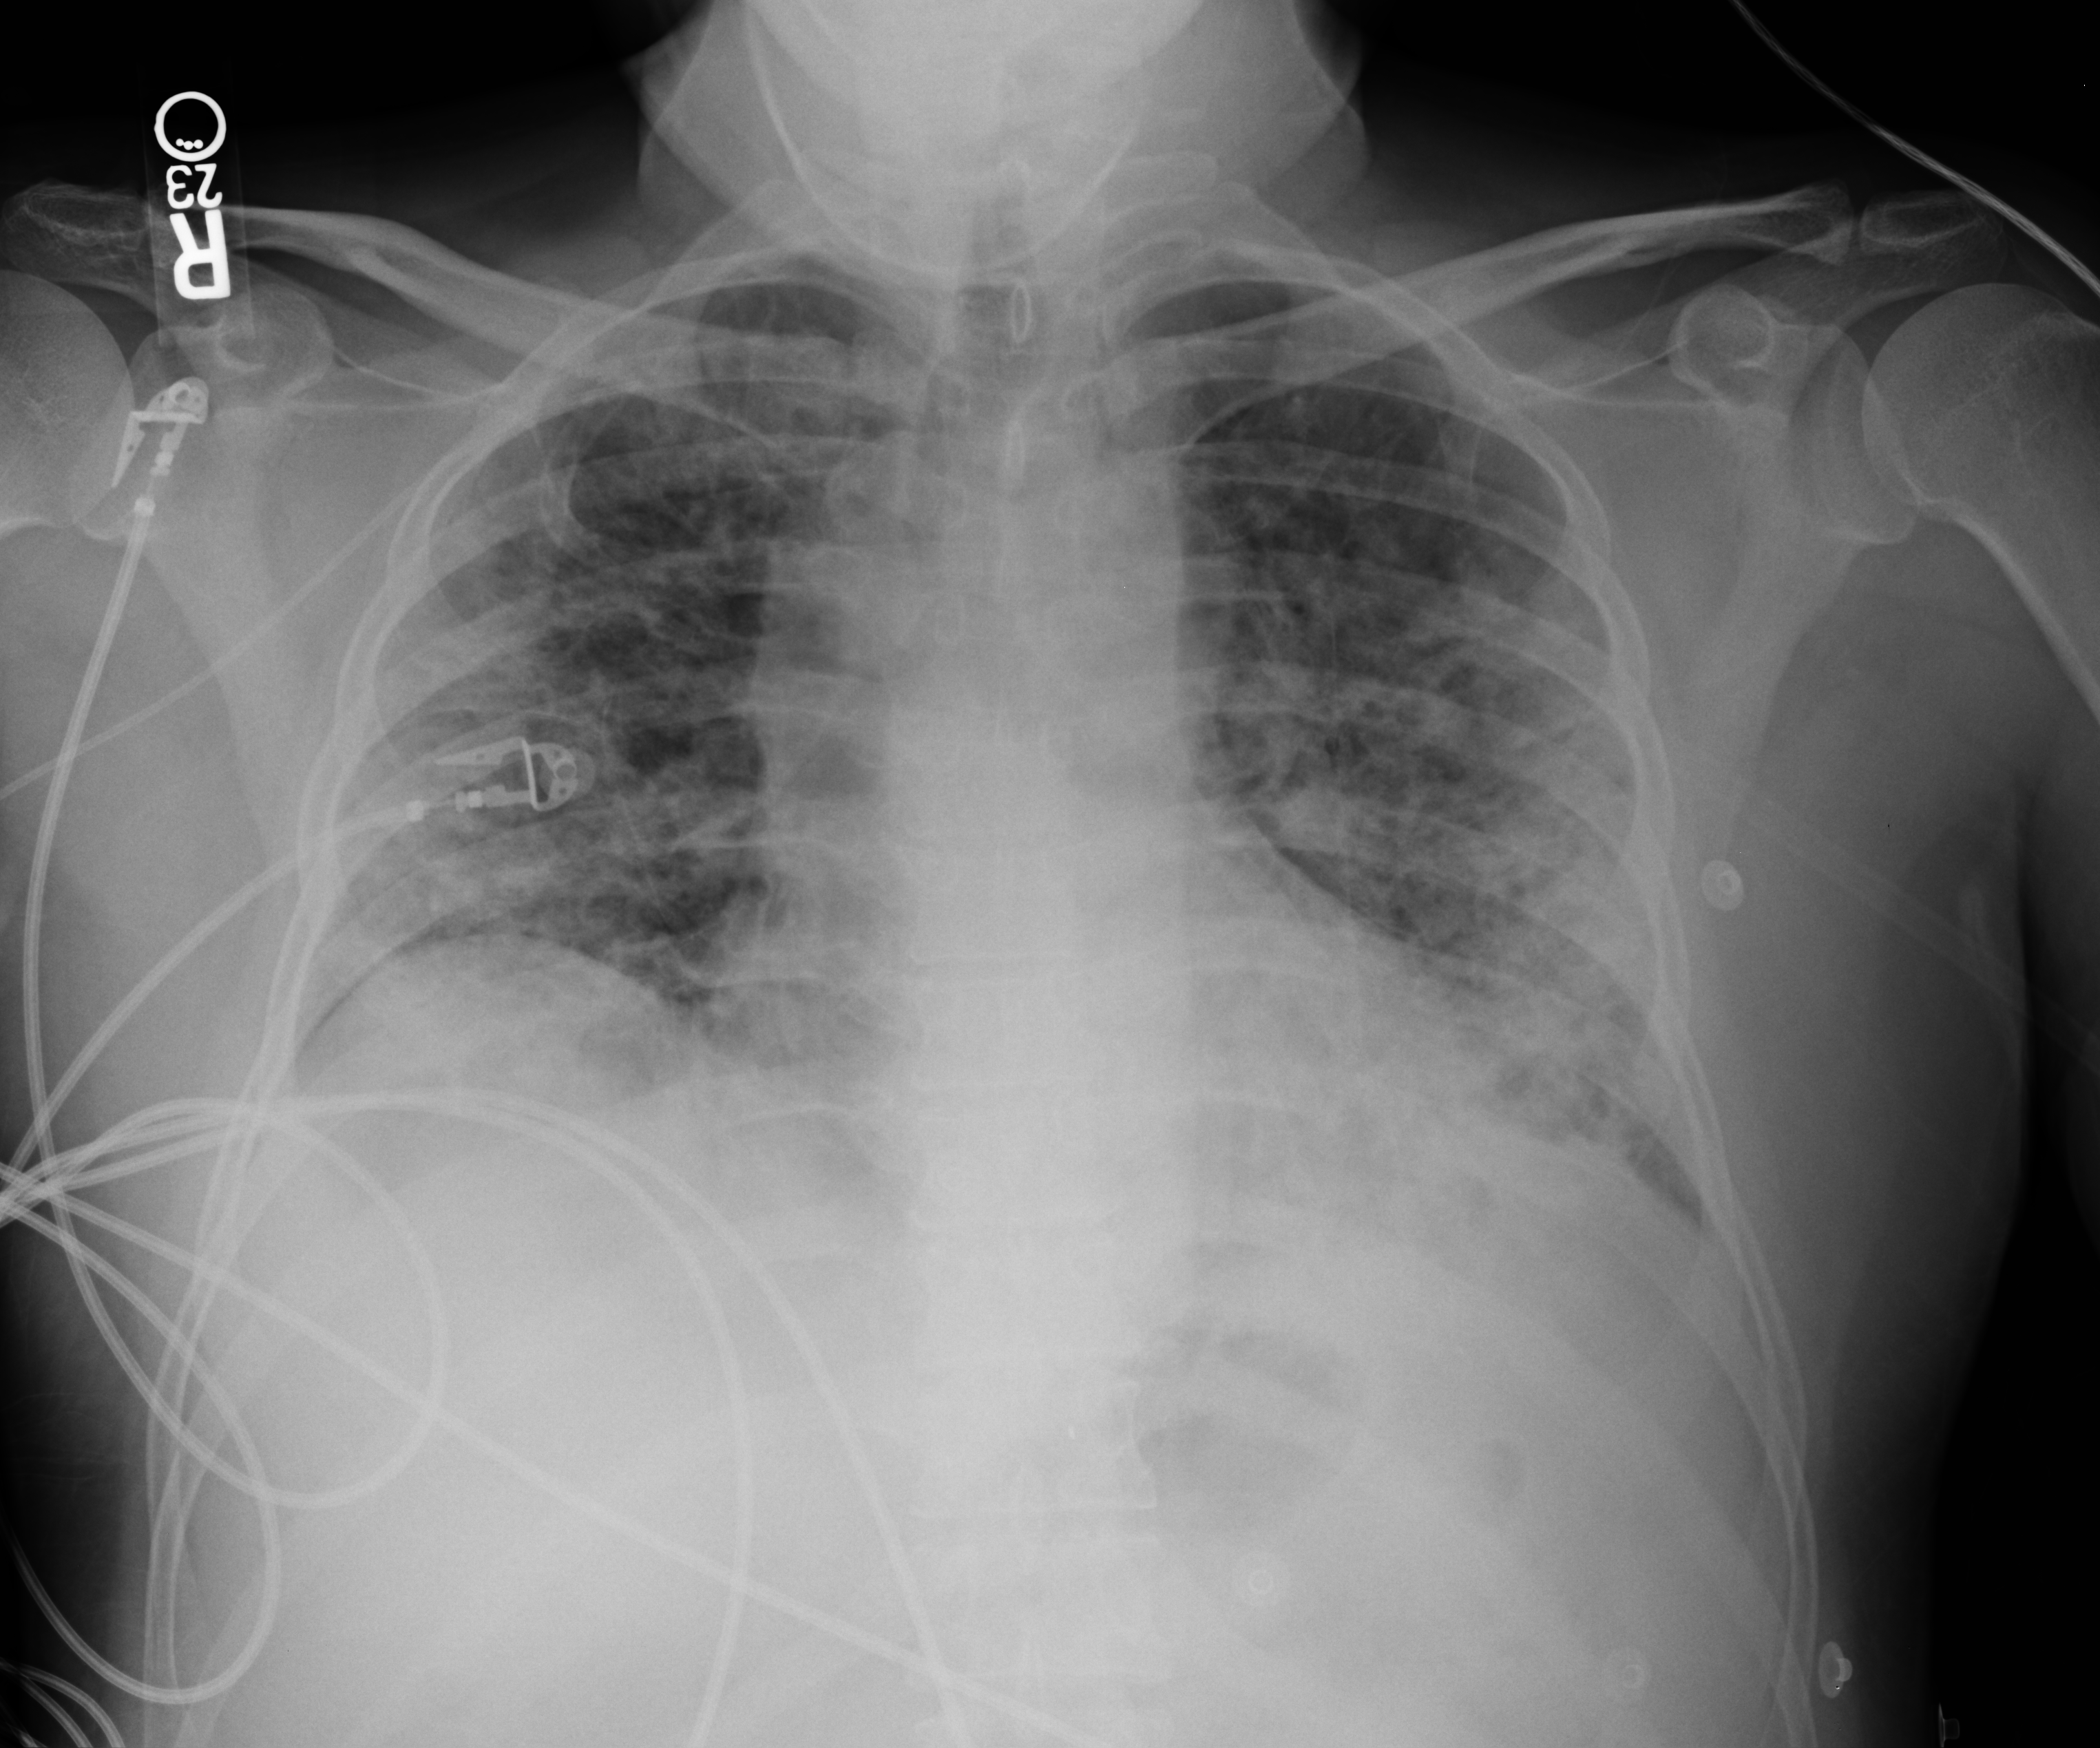
Bedside chest radiograph (computed radiography); anteroposterior (AP) projection. Male patient hospitalised with COVID-19, age 18–59 years.
Admission-level facts for this patient (not findings on this image; timing relative to this image not recorded):
- mechanically ventilated during this hospital stay: no
- admitted to intensive care during this hospital stay: yes